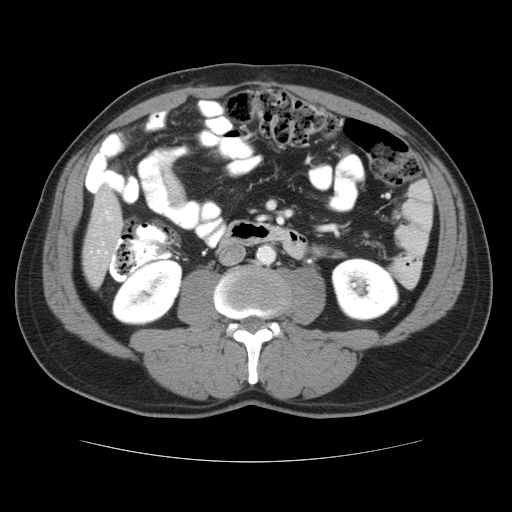
Contrast-enhanced abdominal CT, one axial slice. Slice 8 of 37 in the series (ordered by position). 120 kVp. Intravenous contrast given. Soft-tissue window (W 400 / L 40 HU). 5 mm slice thickness. 512 × 512 image matrix, field of view 374 × 374 mm. Male patient, age 66 years. From the clinical record (not read from this slice): diagnosis: colorectal cancer liver metastases, imaged before liver resection; multiple liver metastases: yes; largest metastasis: 1.6 cm; disease in both lobes: yes.
Annotated regions visible in this slice (outlined manually by an expert reader):
- hepatic veins: bounding box [x1, y1, x2, y2] px = [96, 209, 113, 257]
- liver: [83, 184, 123, 287]
- planned liver remnant (the part of the liver to remain after resection): [83, 184, 123, 287]
- liver metastasis: [100, 227, 108, 236]